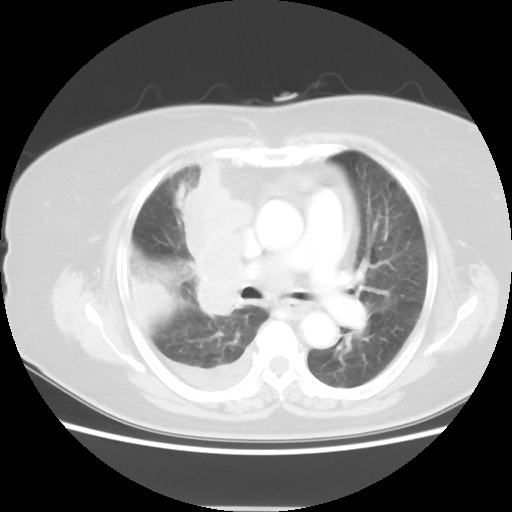
Chest CT, one axial slice; slice 30 of 48 in the series (ordered by position); lung window (W 1500 / L -600 HU); 5 mm slice thickness; 512 × 512 image matrix, field of view 360 × 360 mm. Female patient, age 73 years. Case-level facts recorded for this patient, not image findings: clinical TNM (as recorded): T3 N3 M1b; histopathological grade: G3.
Outlined on this slice (bounding box drawn by a radiologist):
- lung tumour (recorded histology: small cell carcinoma): bounding box (x1, y1, x2, y2) in pixels: (182, 162, 252, 314)